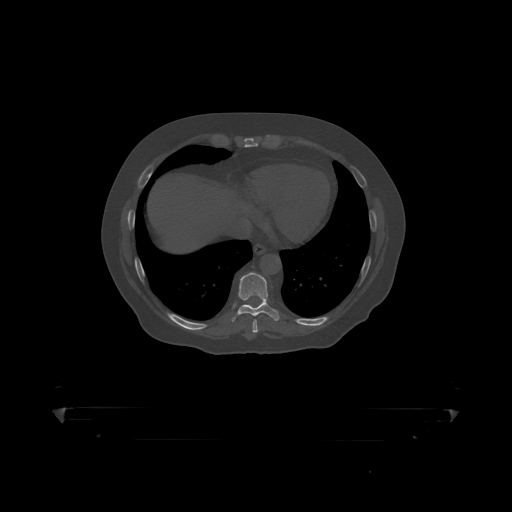
CT including the spine, one axial slice. Position 238 of 390 along the scan axis. Reconstruction kernel STANDARD. 120 kVp. Bone window (W 1800 / L 400 HU). 1.25 mm slice thickness. 512 × 512 image matrix. Male patient, age 60 years. Case-level facts recorded for this patient, not image findings: primary cancer: prostate.
Structures marked on this image (semi-automatically segmented with operator editing):
- T9 vertebra: bounding box (x1, y1, x2, y2) in pixels: (234, 273, 280, 317)